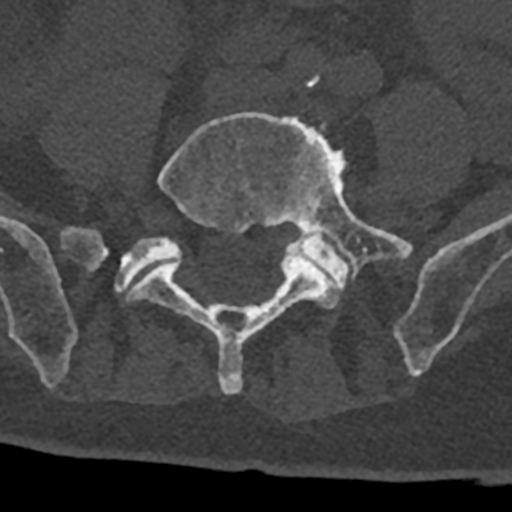
CT including the spine, one axial slice. Slice 194 of 797 in the series (ordered by position). Reconstruction kernel Br40s/3. Bone window (W 1800 / L 400 HU). 512 × 512 image matrix. Male patient, age 74 years. From the clinical record (not read from this slice): primary cancer: renal; vertebrae with lytic lesions (as recorded): T10, L1, L2, L3, L4, L5.
Structures marked on this image (semi-automatically segmented with operator editing):
- L5 vertebra: bounding box <126,112,412,394> (left, top, right, bottom; pixels)